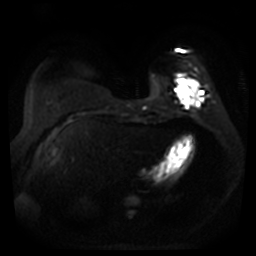
Breast MRI, one axial slice; slice 10 of 44 in the series (ordered by position); diffusion-weighted series; image 2 of 4 stored at this slice position (different b-values; order by instance number); 3 T; 5 mm slice thickness; 256 × 256 image matrix. Female patient.
Annotated regions visible in this slice (outlined manually by an expert reader):
- tumour on diffusion-weighted imaging: bounding box <177,78,200,105> (left, top, right, bottom; pixels)